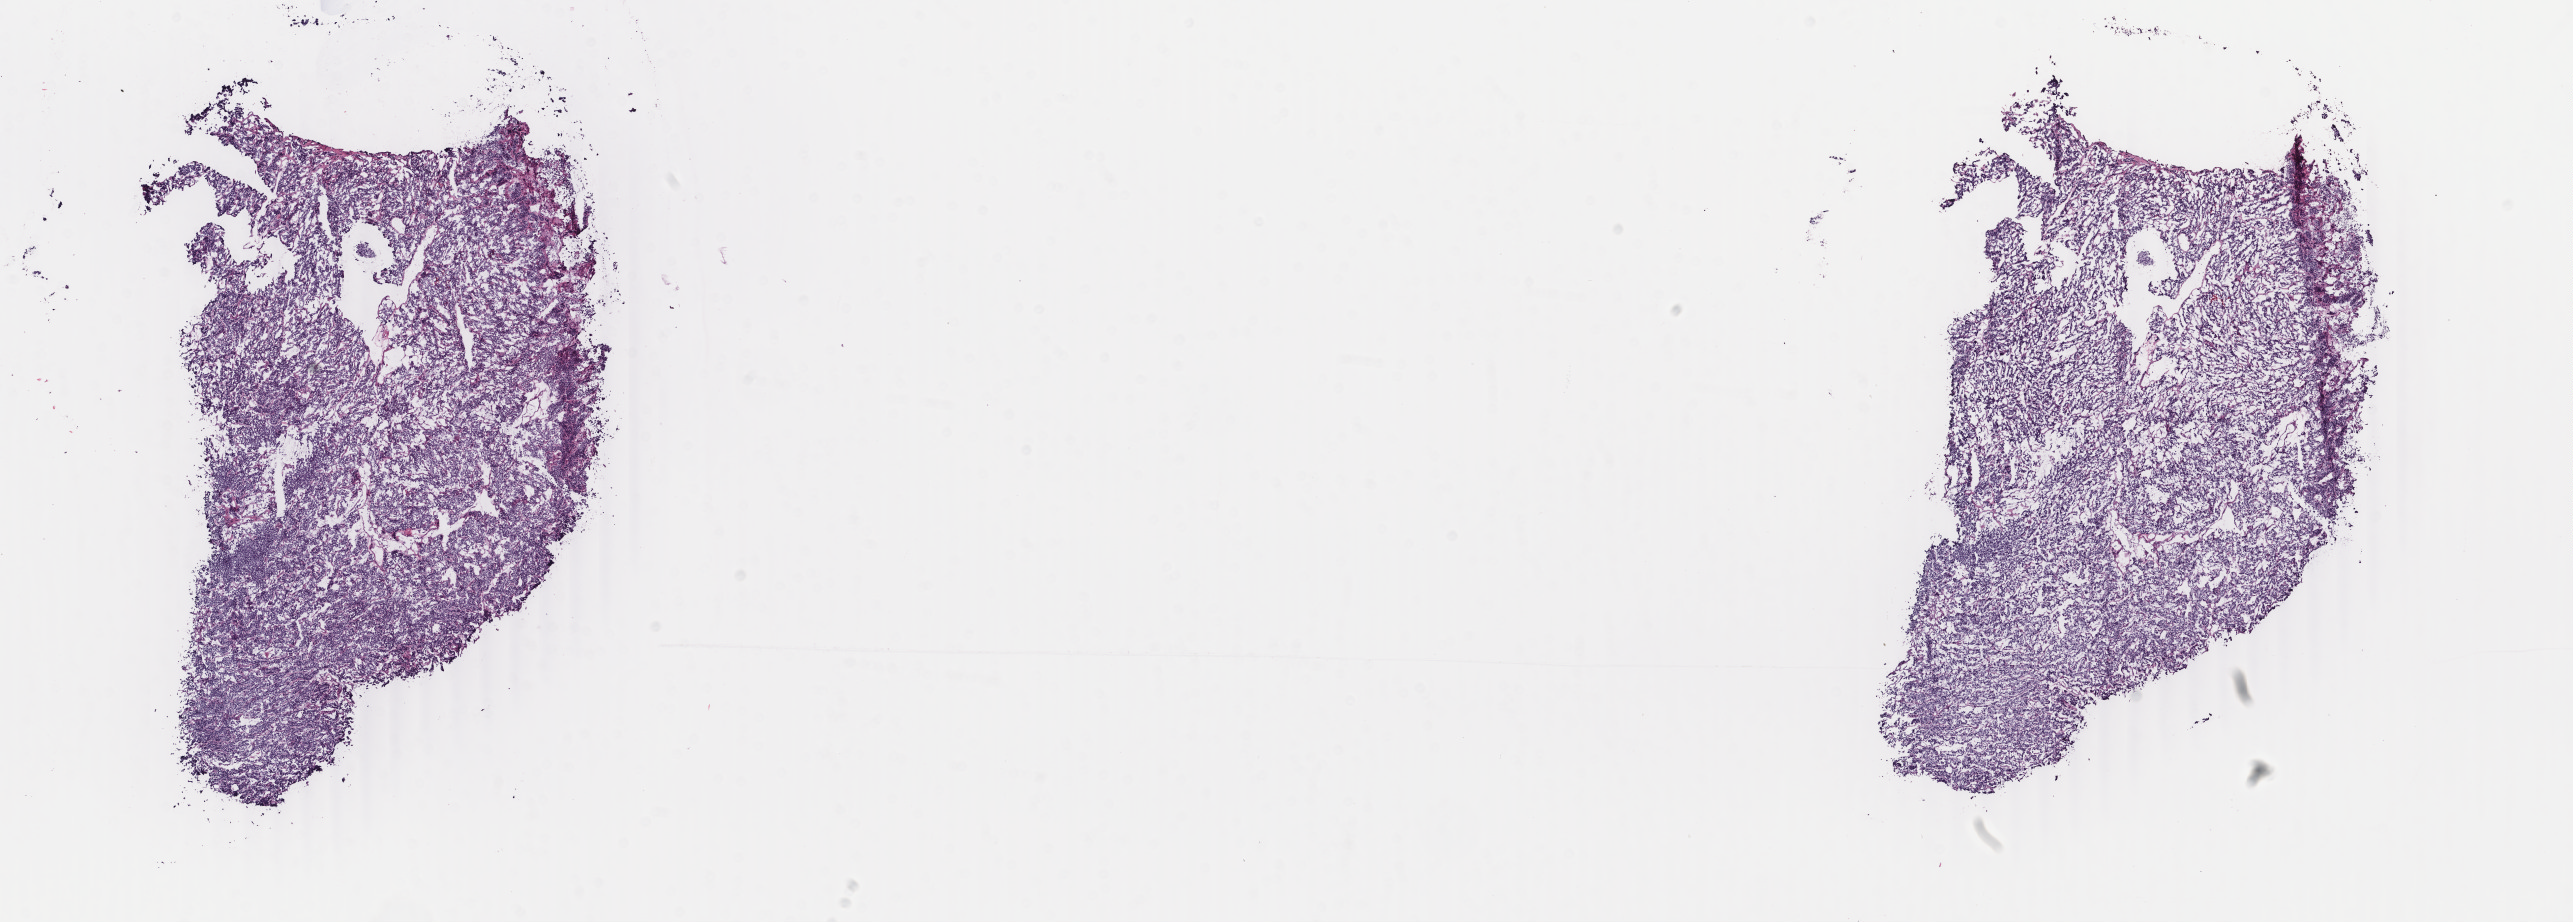
Hematoxylin and eosin (H&E) stained whole-slide image, whole scanned area (about 20.5 x 7.3 mm) shown as a low-resolution overview, frozen section, thyroid, primary tumour sample. Patient: female, age at initial diagnosis 52 years. Pathologist review of this section (percent, as recorded): tumour cells 100%, tumour nuclei 98%, normal cells 0%, stromal cells 0%, necrosis 0%. Inflammatory infiltration, as recorded: lymphocyte infiltration 0%, monocyte infiltration 0%, neutrophil infiltration 0%.
Laterality: right. TNM: T2 N0 M0. AJCC pathologic stage: II. Pathologic diagnosis: Papillary adenocarcinoma, NOS (thyroid gland).